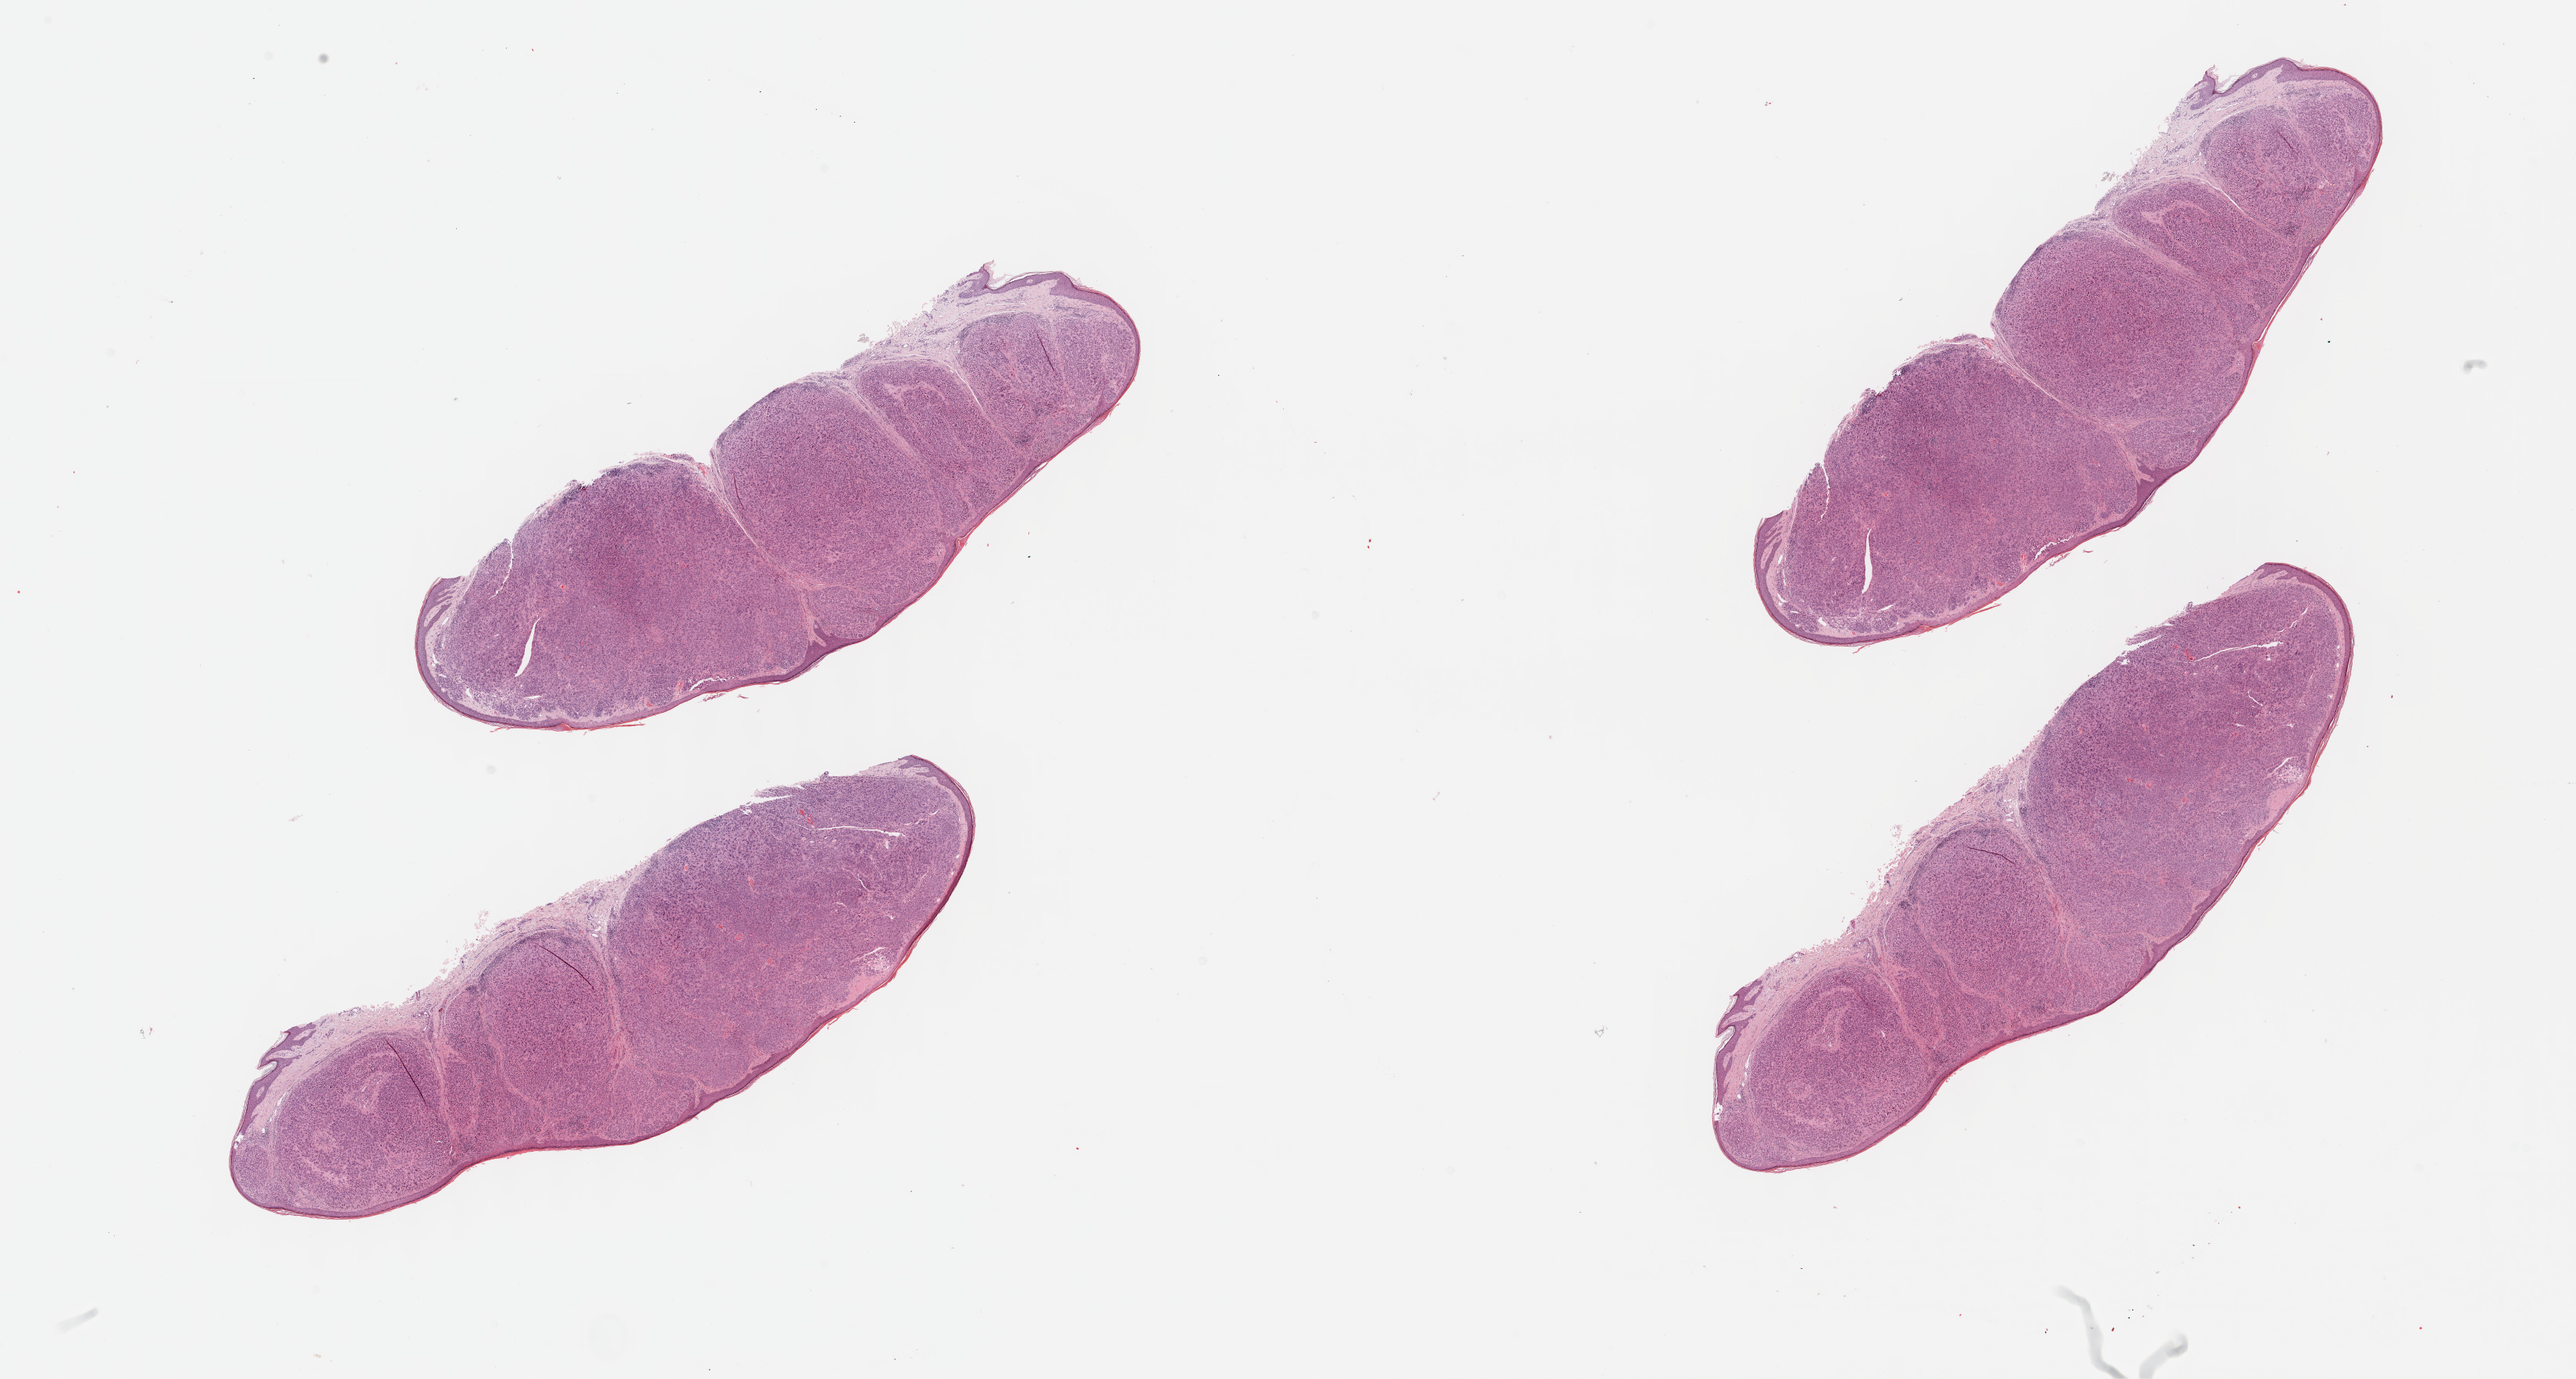
Whole-slide histology image, H&E-stained — a low-resolution overview of the entire scanned area, about 26.7 x 14.3 mm, FFPE section, metastatic tumour sample, sampled site not recorded. Patient: male, age at initial diagnosis 62 years.
* this section: metastatic tumour tissue
* patient diagnosis: Malignant melanoma, NOS